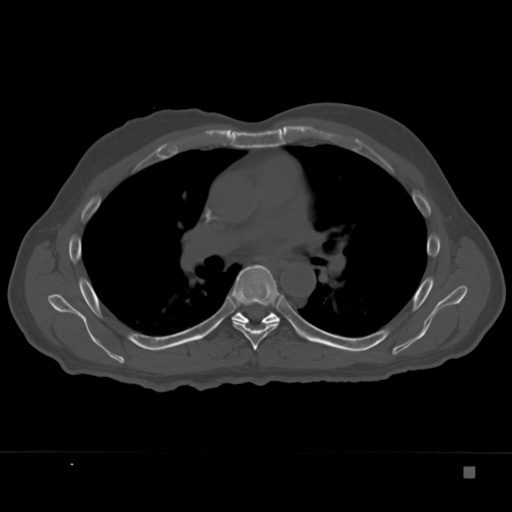
CT including the spine, one axial slice. Position 234 of 332 along the scan axis. 120 kVp. Bone window (W 1800 / L 400 HU). 1.5 mm slice thickness. 512 × 512 image matrix, field of view 389 × 389 mm. Male patient, age 72 years. Case-level facts recorded for this patient, not image findings: primary cancer: skeletal.
Structures marked on this image (semi-automatically segmented with operator editing):
- T6 vertebra: box from (x=230, y=265) to (x=284, y=351) px
- T7 vertebra: (x=232, y=311)–(x=280, y=324)